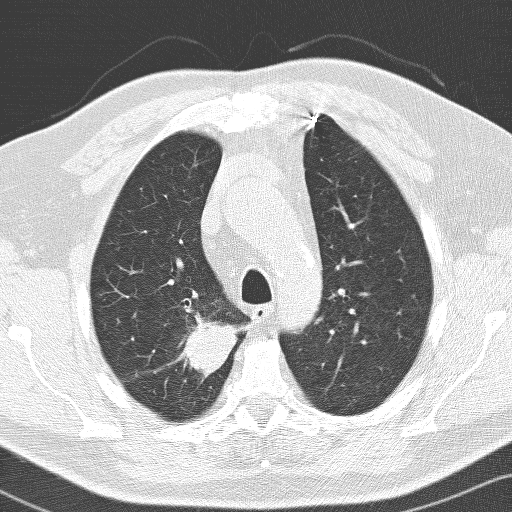
Low-dose screening chest CT, axial slice; baseline screening round; lung window (W 1500 / L -600 HU); 512 × 512 image matrix, field of view 326 × 326 mm. Male participant, aged 66 years at enrolment.
Lesion marked by an expert reader, bounding box [x1, y1, x2, y2] px = [151, 307, 232, 392]. Reader record for this screening exam (exam-level; its link to the box is not recorded): non-calcified nodule or mass ≥4 mm, right upper lobe, 36 × 30 mm, spiculated (stellate) margins, soft tissue attenuation. Later outcome: lung cancer diagnosed 103 days after this screen — adenocarcinoma, NOS, right upper lobe, poorly differentiated (G3), stage IIB (AJCC 6th edition), 33 mm at pathology.